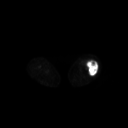
FDG PET of an extremity soft-tissue mass (from a PET/CT study), one axial slice; slice 209 of 267 in the series (ordered by position); 3.27 mm slice thickness; 128 × 128 image matrix. Female patient, age 62 years. From the clinical record (not read from this slice): histological type: undifferentiated – high grade; grade: high; site of the primary tumour: left thigh.
Outlined on this slice (expert contour drawn on MRI and transferred to this co-registered scan by the dataset authors):
- gross tumour volume including surrounding oedema: bounding box (x1, y1, x2, y2) in pixels: (83, 59, 98, 75)
- gross tumour volume (mass): (86, 59, 98, 75)